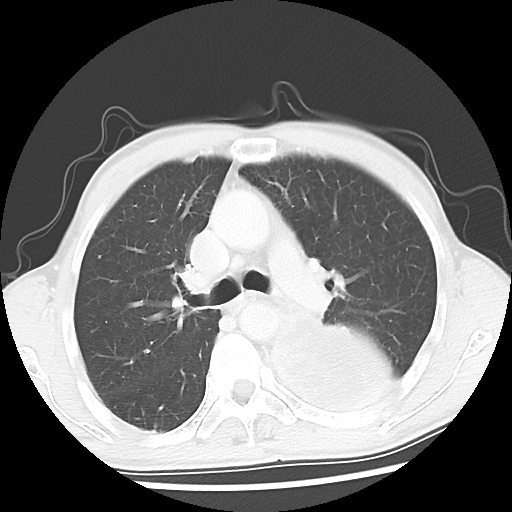
Chest CT, one axial slice; position 33 of 52 along the scan axis; reconstruction kernel LUNG; 120 kVp; lung window (W 1500 / L -600 HU); 512 × 512 image matrix, field of view 318 × 318 mm. Patient: male, 60 years. From the clinical record (not read from this slice): clinical TNM (as recorded): T4 N0 M0.
Annotated regions visible in this slice (rectangle marked by the reading radiologist):
- lung tumour (recorded histology: squamous cell carcinoma): box from (x=268, y=311) to (x=410, y=428) px